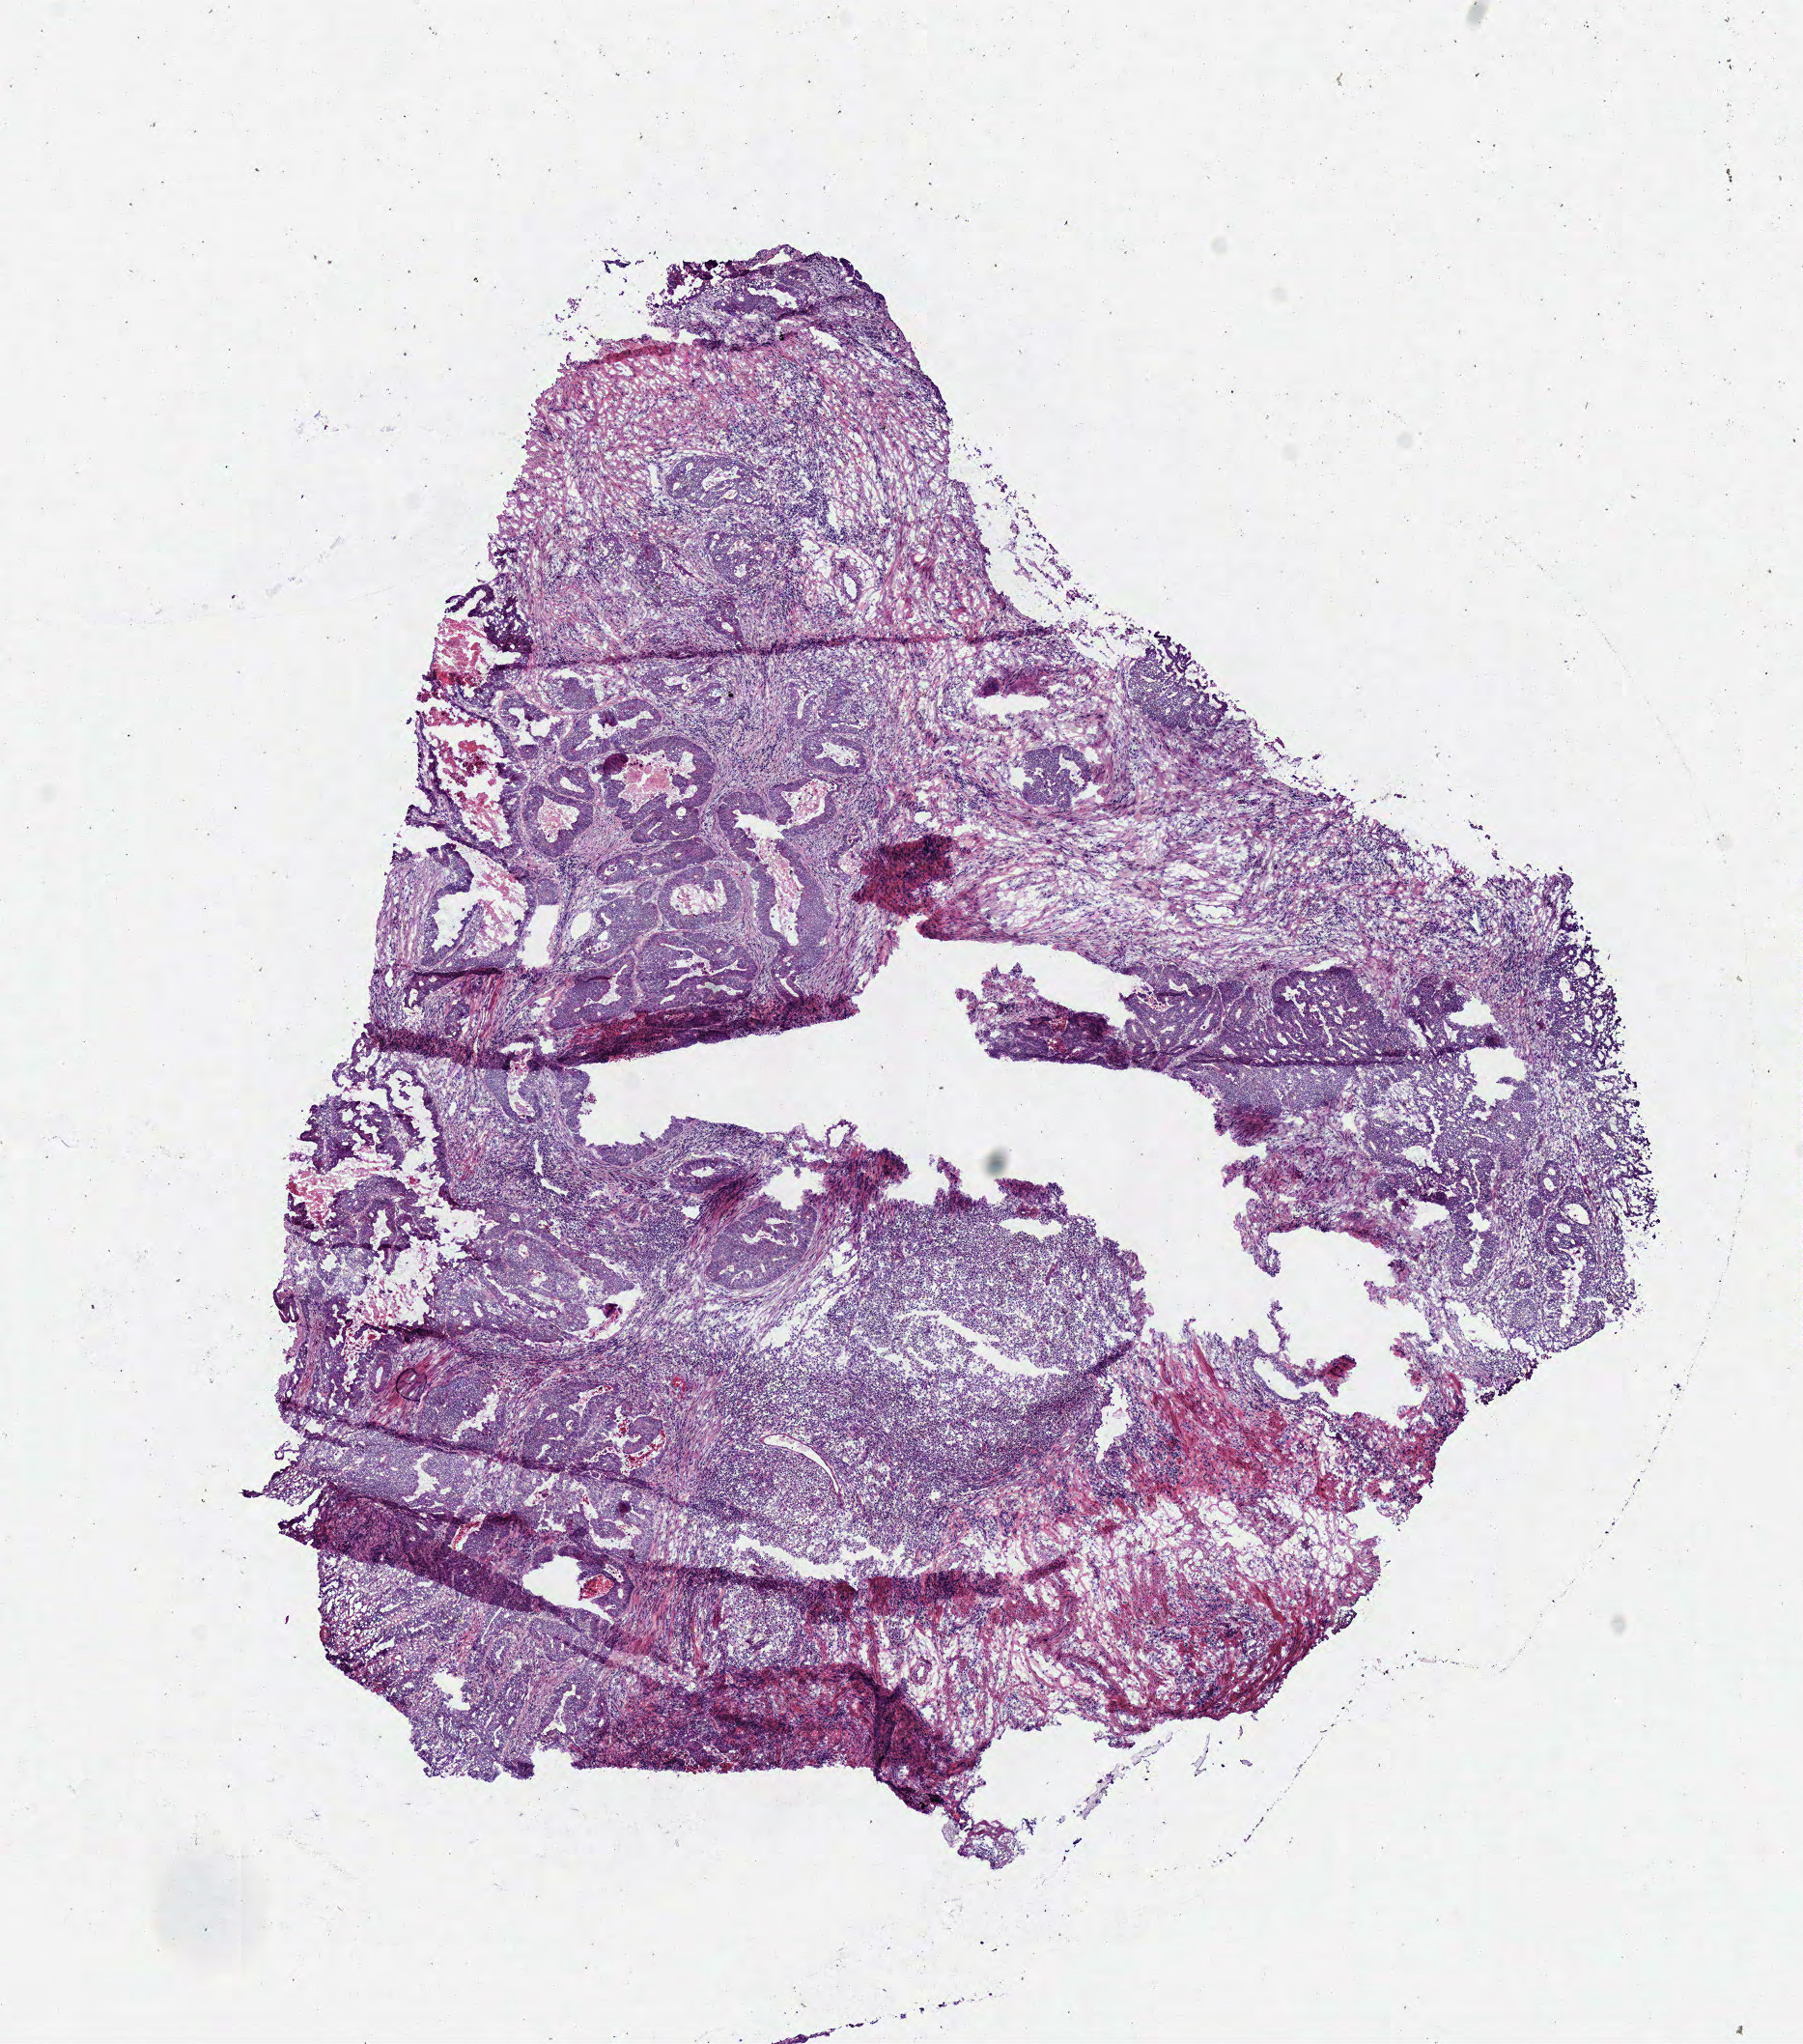
H&E whole-slide image, shown as a low-resolution overview of the whole scanned area (about 7.3 x 8.3 mm); frozen section from the bottom of the tissue portion; sample: primary tumour, colon. Male patient; age at initial diagnosis 61 years. Composition of this section per pathologist review: tumour cells 75%, tumour nuclei 60%, normal cells 0%, stromal cells 20%, necrosis 5%. Infiltration values recorded for this section: lymphocyte infiltration 15%, monocyte infiltration 0%, neutrophil infiltration 15%.
- diagnosis: Adenocarcinoma, NOS (sigmoid colon)
- TNM: T3 N0 M0
- lymph nodes positive (case pathology): 0 of 10 examined
- AJCC pathologic stage: IIA